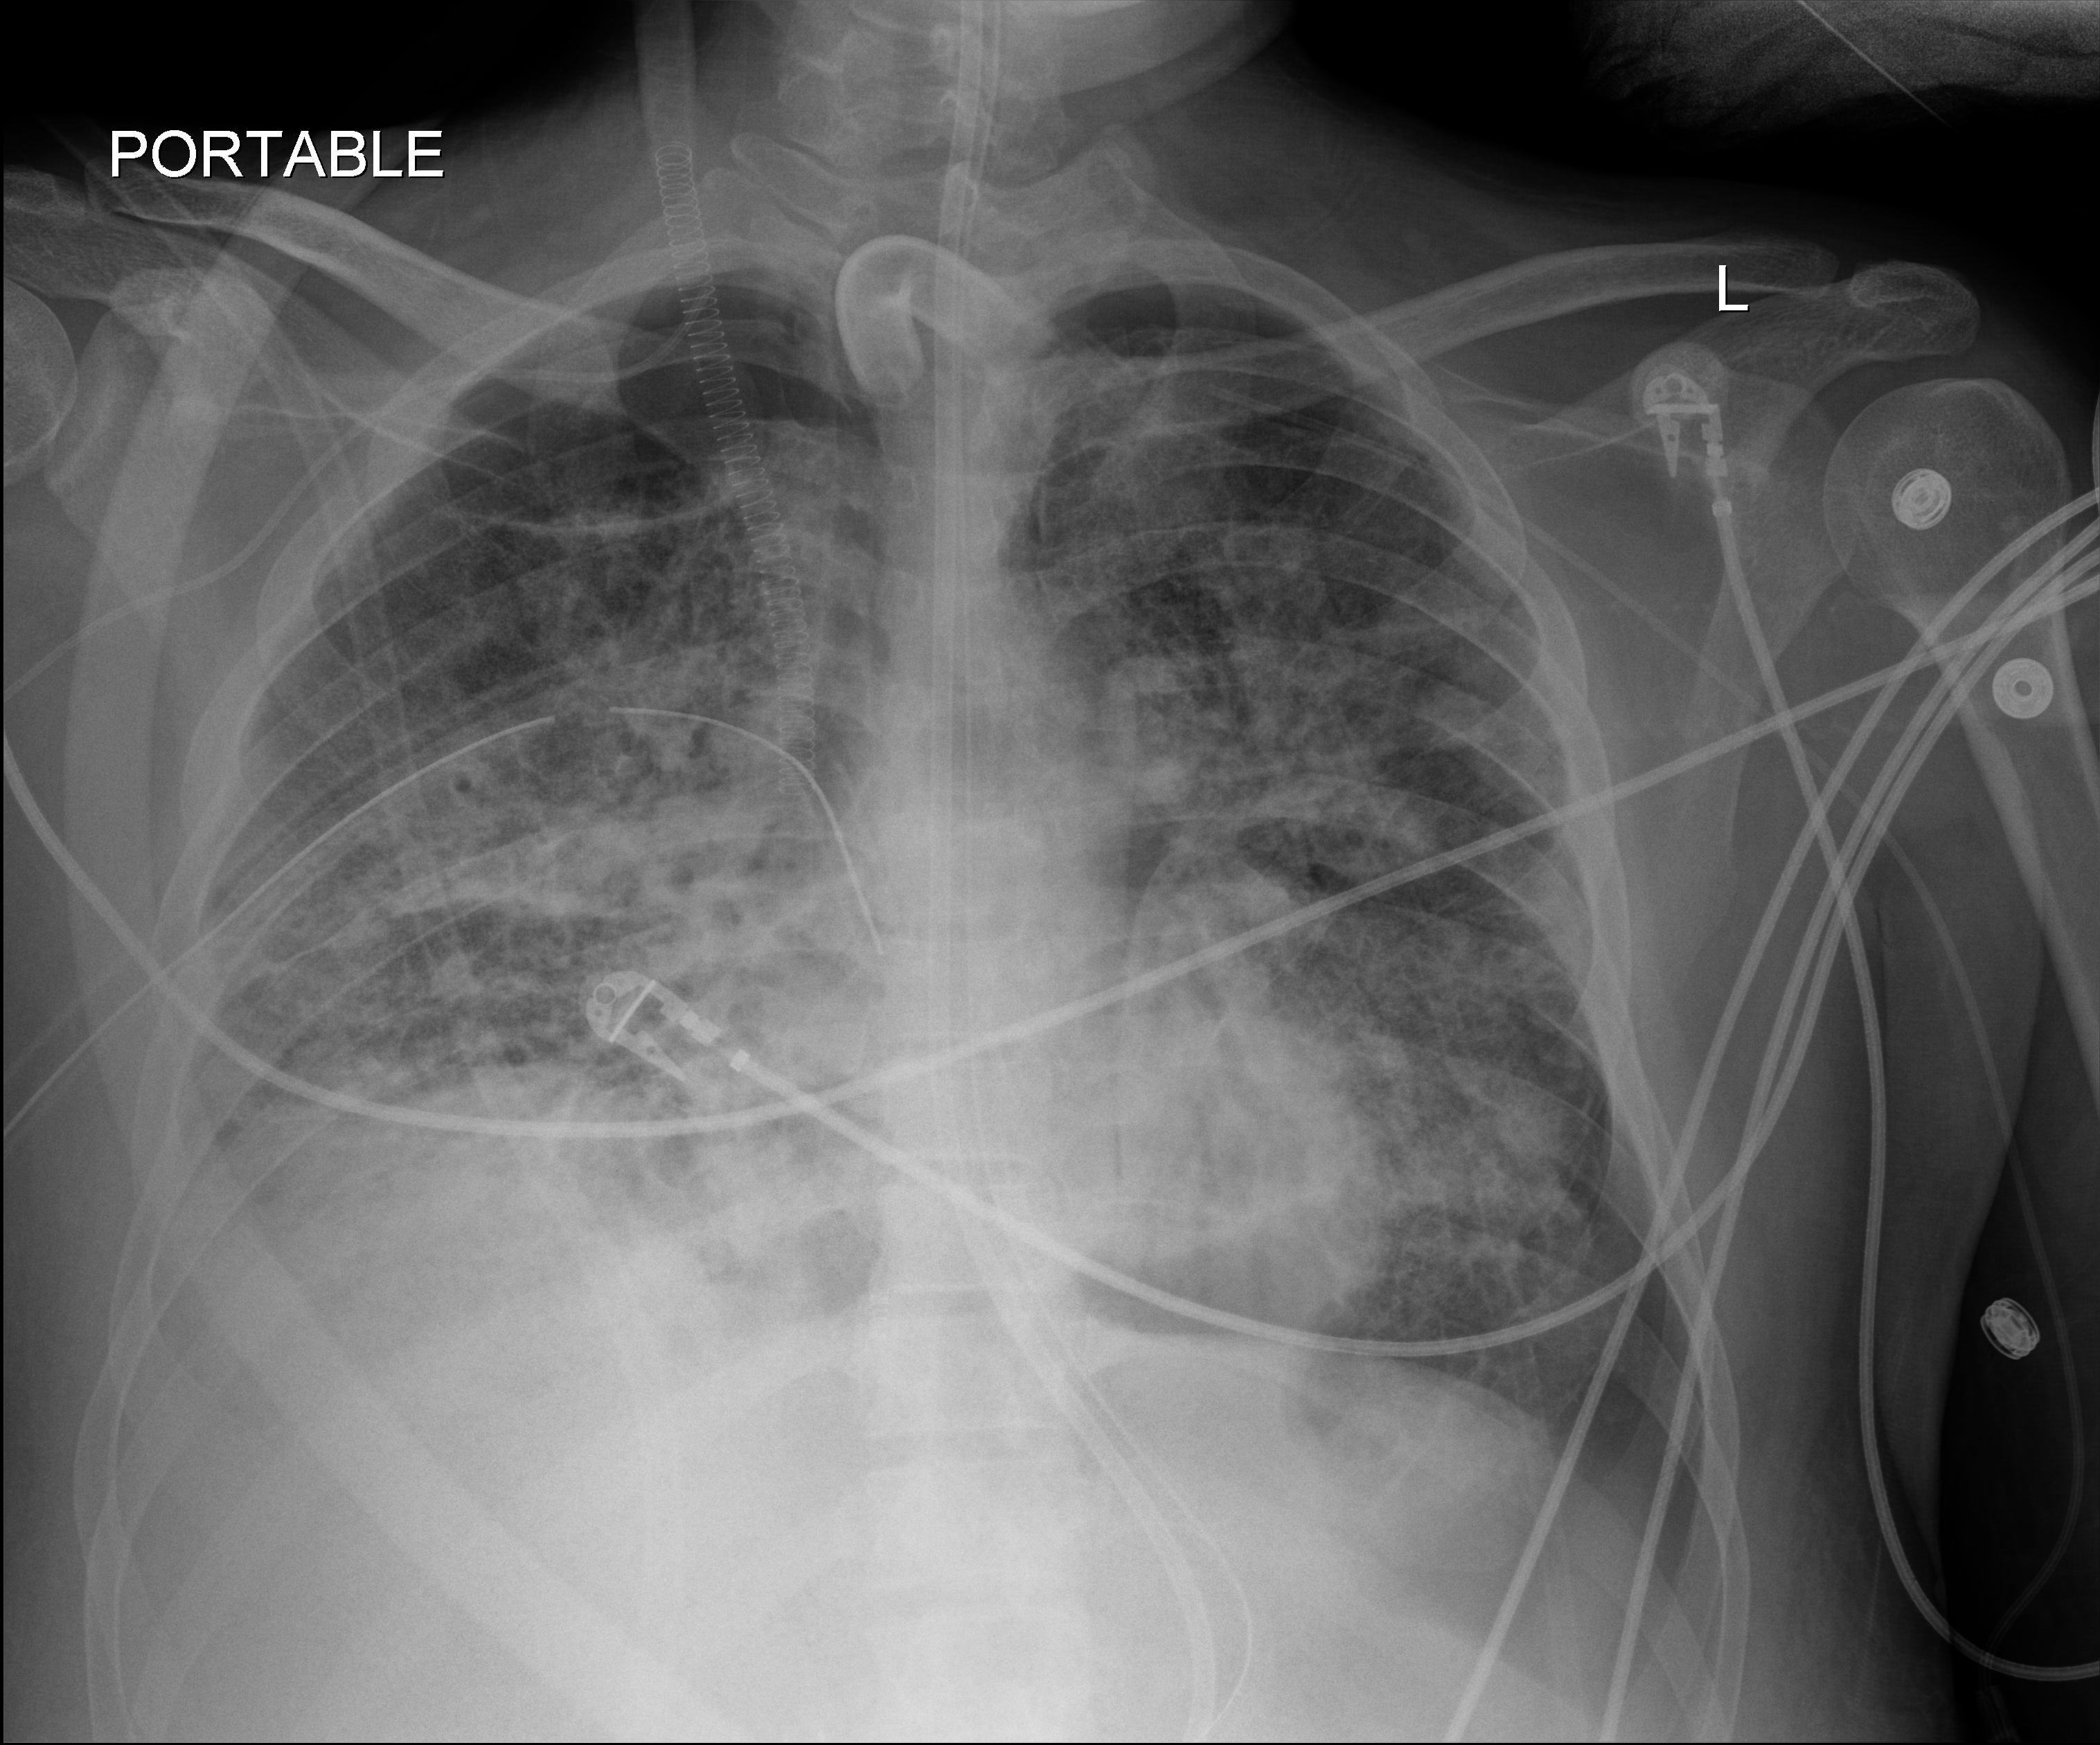
Bedside chest radiograph (digital radiography). Patient hospitalised with COVID-19, aged 18–59 years.
From the hospital-stay record, not from the radiograph (when in the stay this image was taken is not recorded): smoking status (admission record): never; mechanically ventilated during this hospital stay: yes.